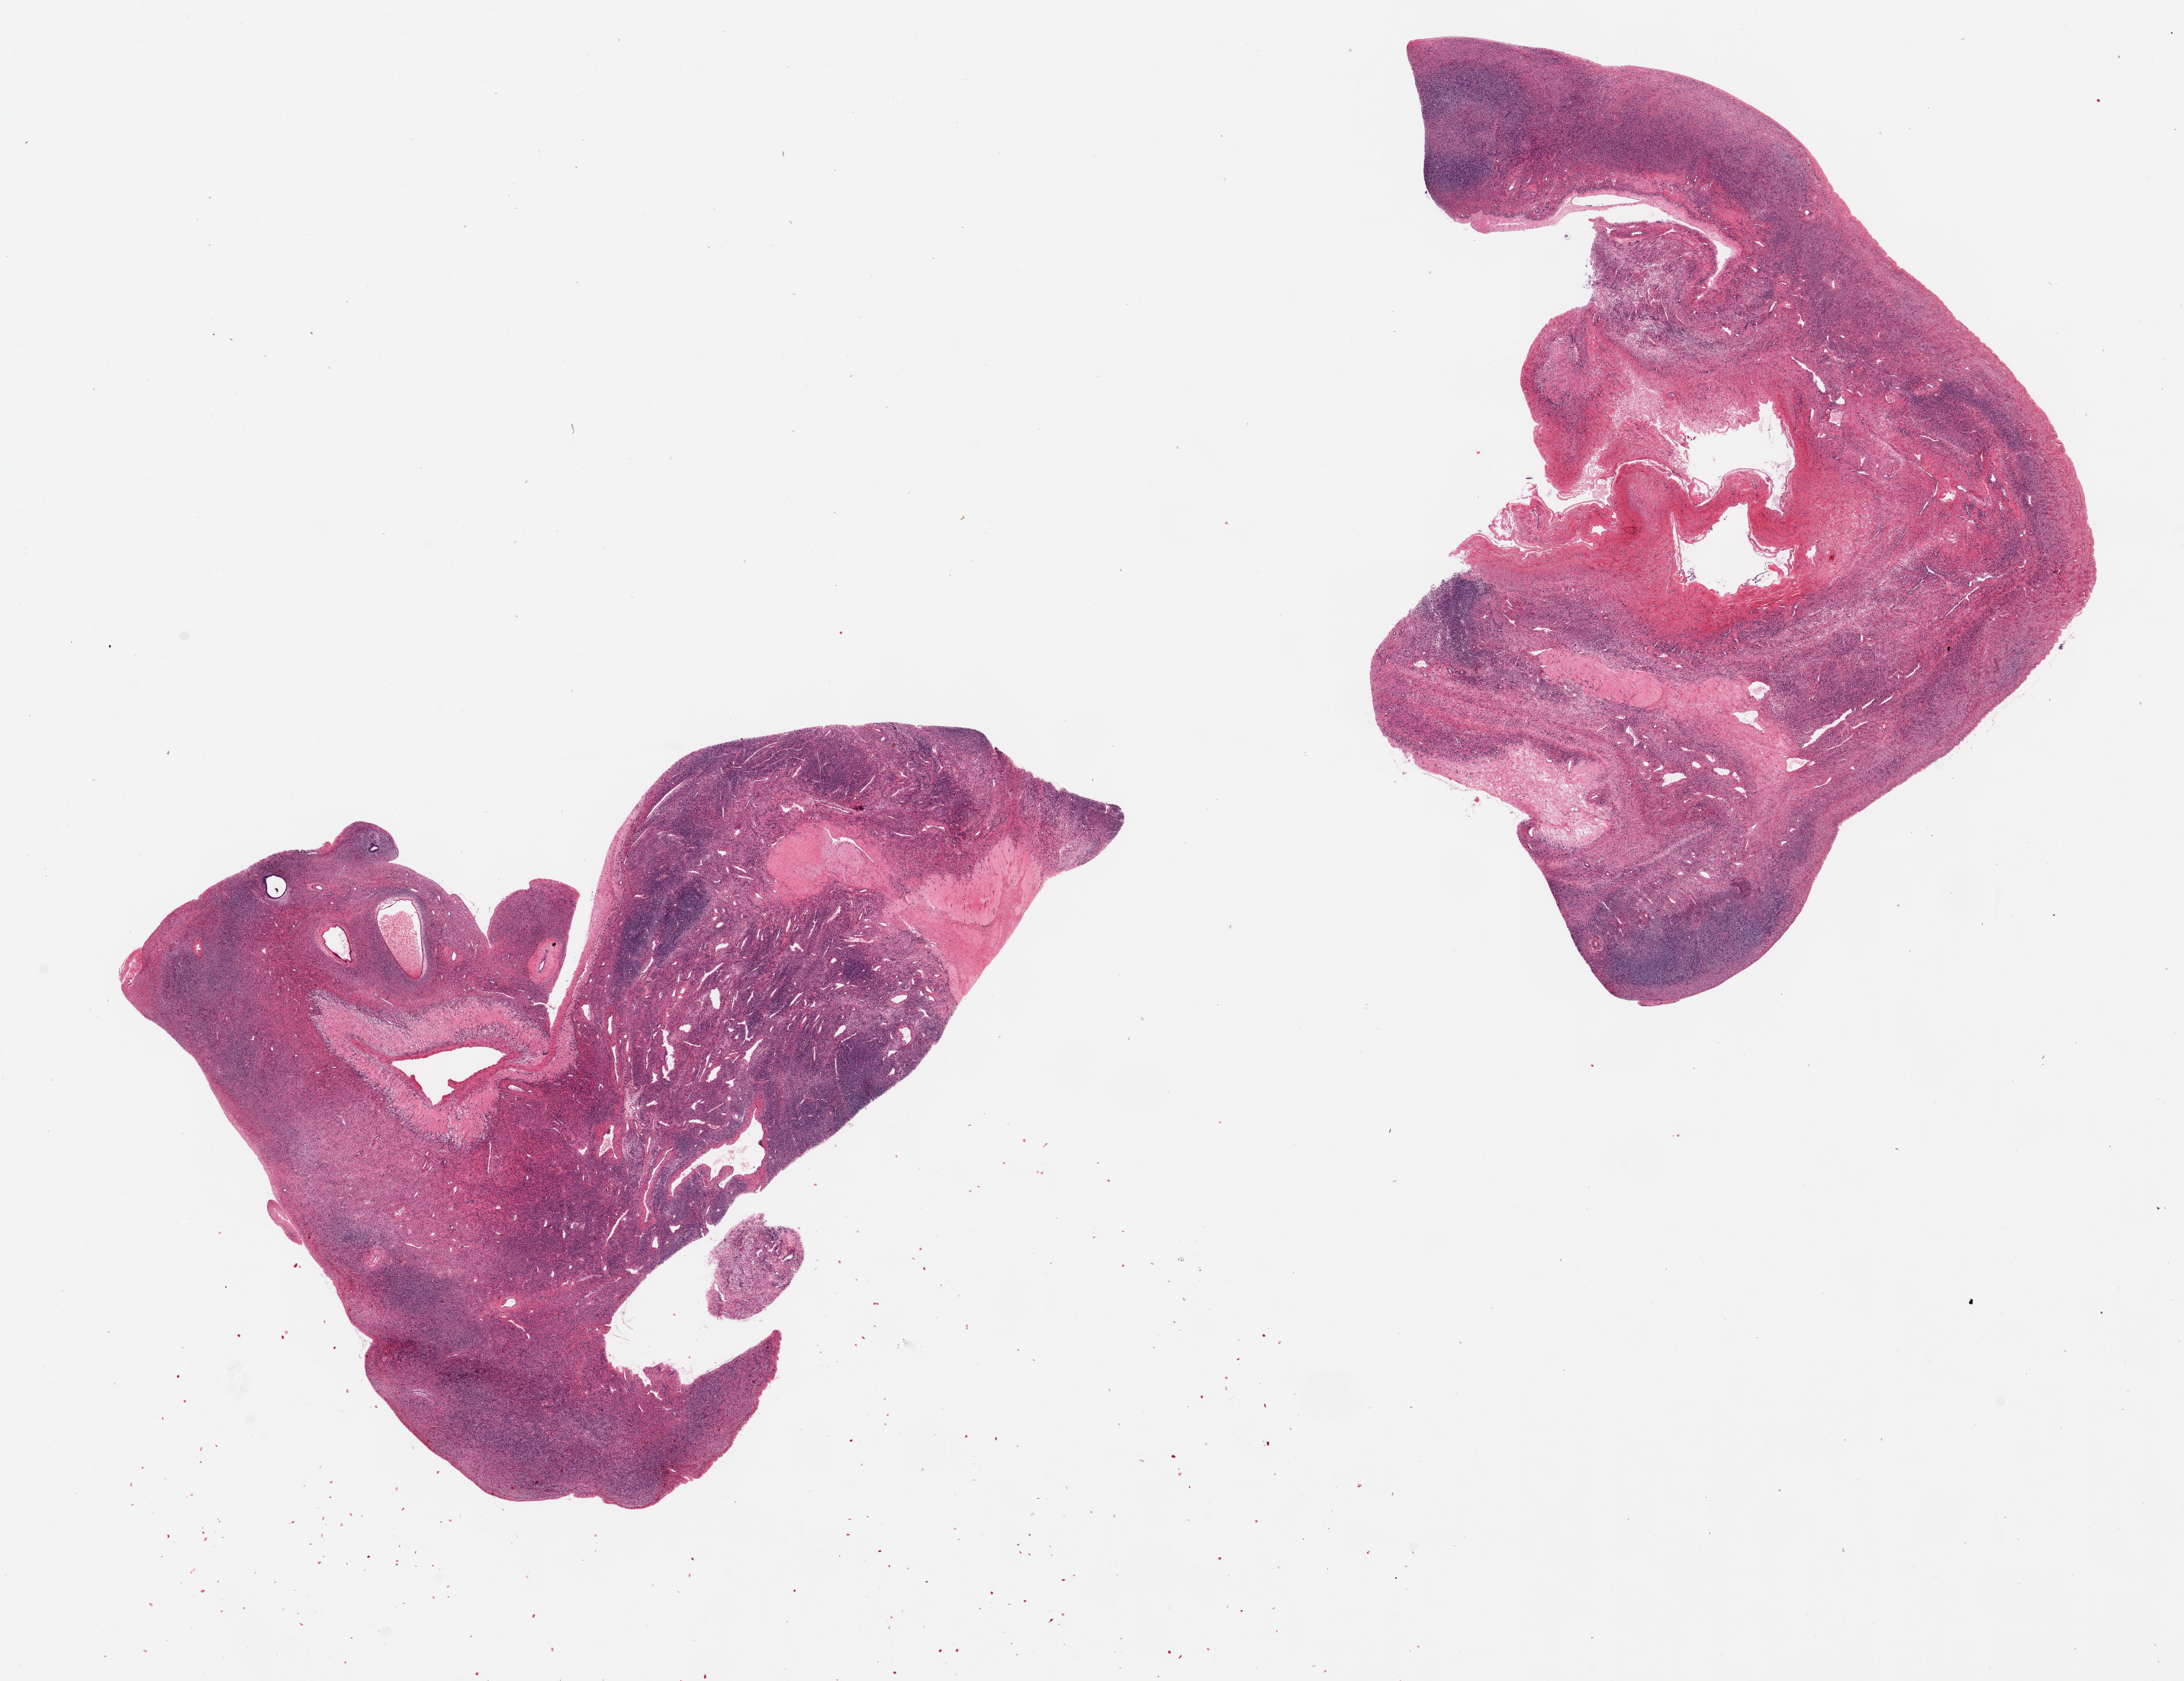
Haematoxylin and eosin whole-slide image, low-resolution overview of the scanned area, about 22.6 x 17.4 mm (from a 20x scan); PAXgene-fixed paraffin-embedded (PFPE) section; target tissue: ovary; tissue donor sample. Donor sex: female.
Reviewer comment on this tissue sample: 2 pieces, 9x7 & 10x9mm; various corpora; no obvious ova.